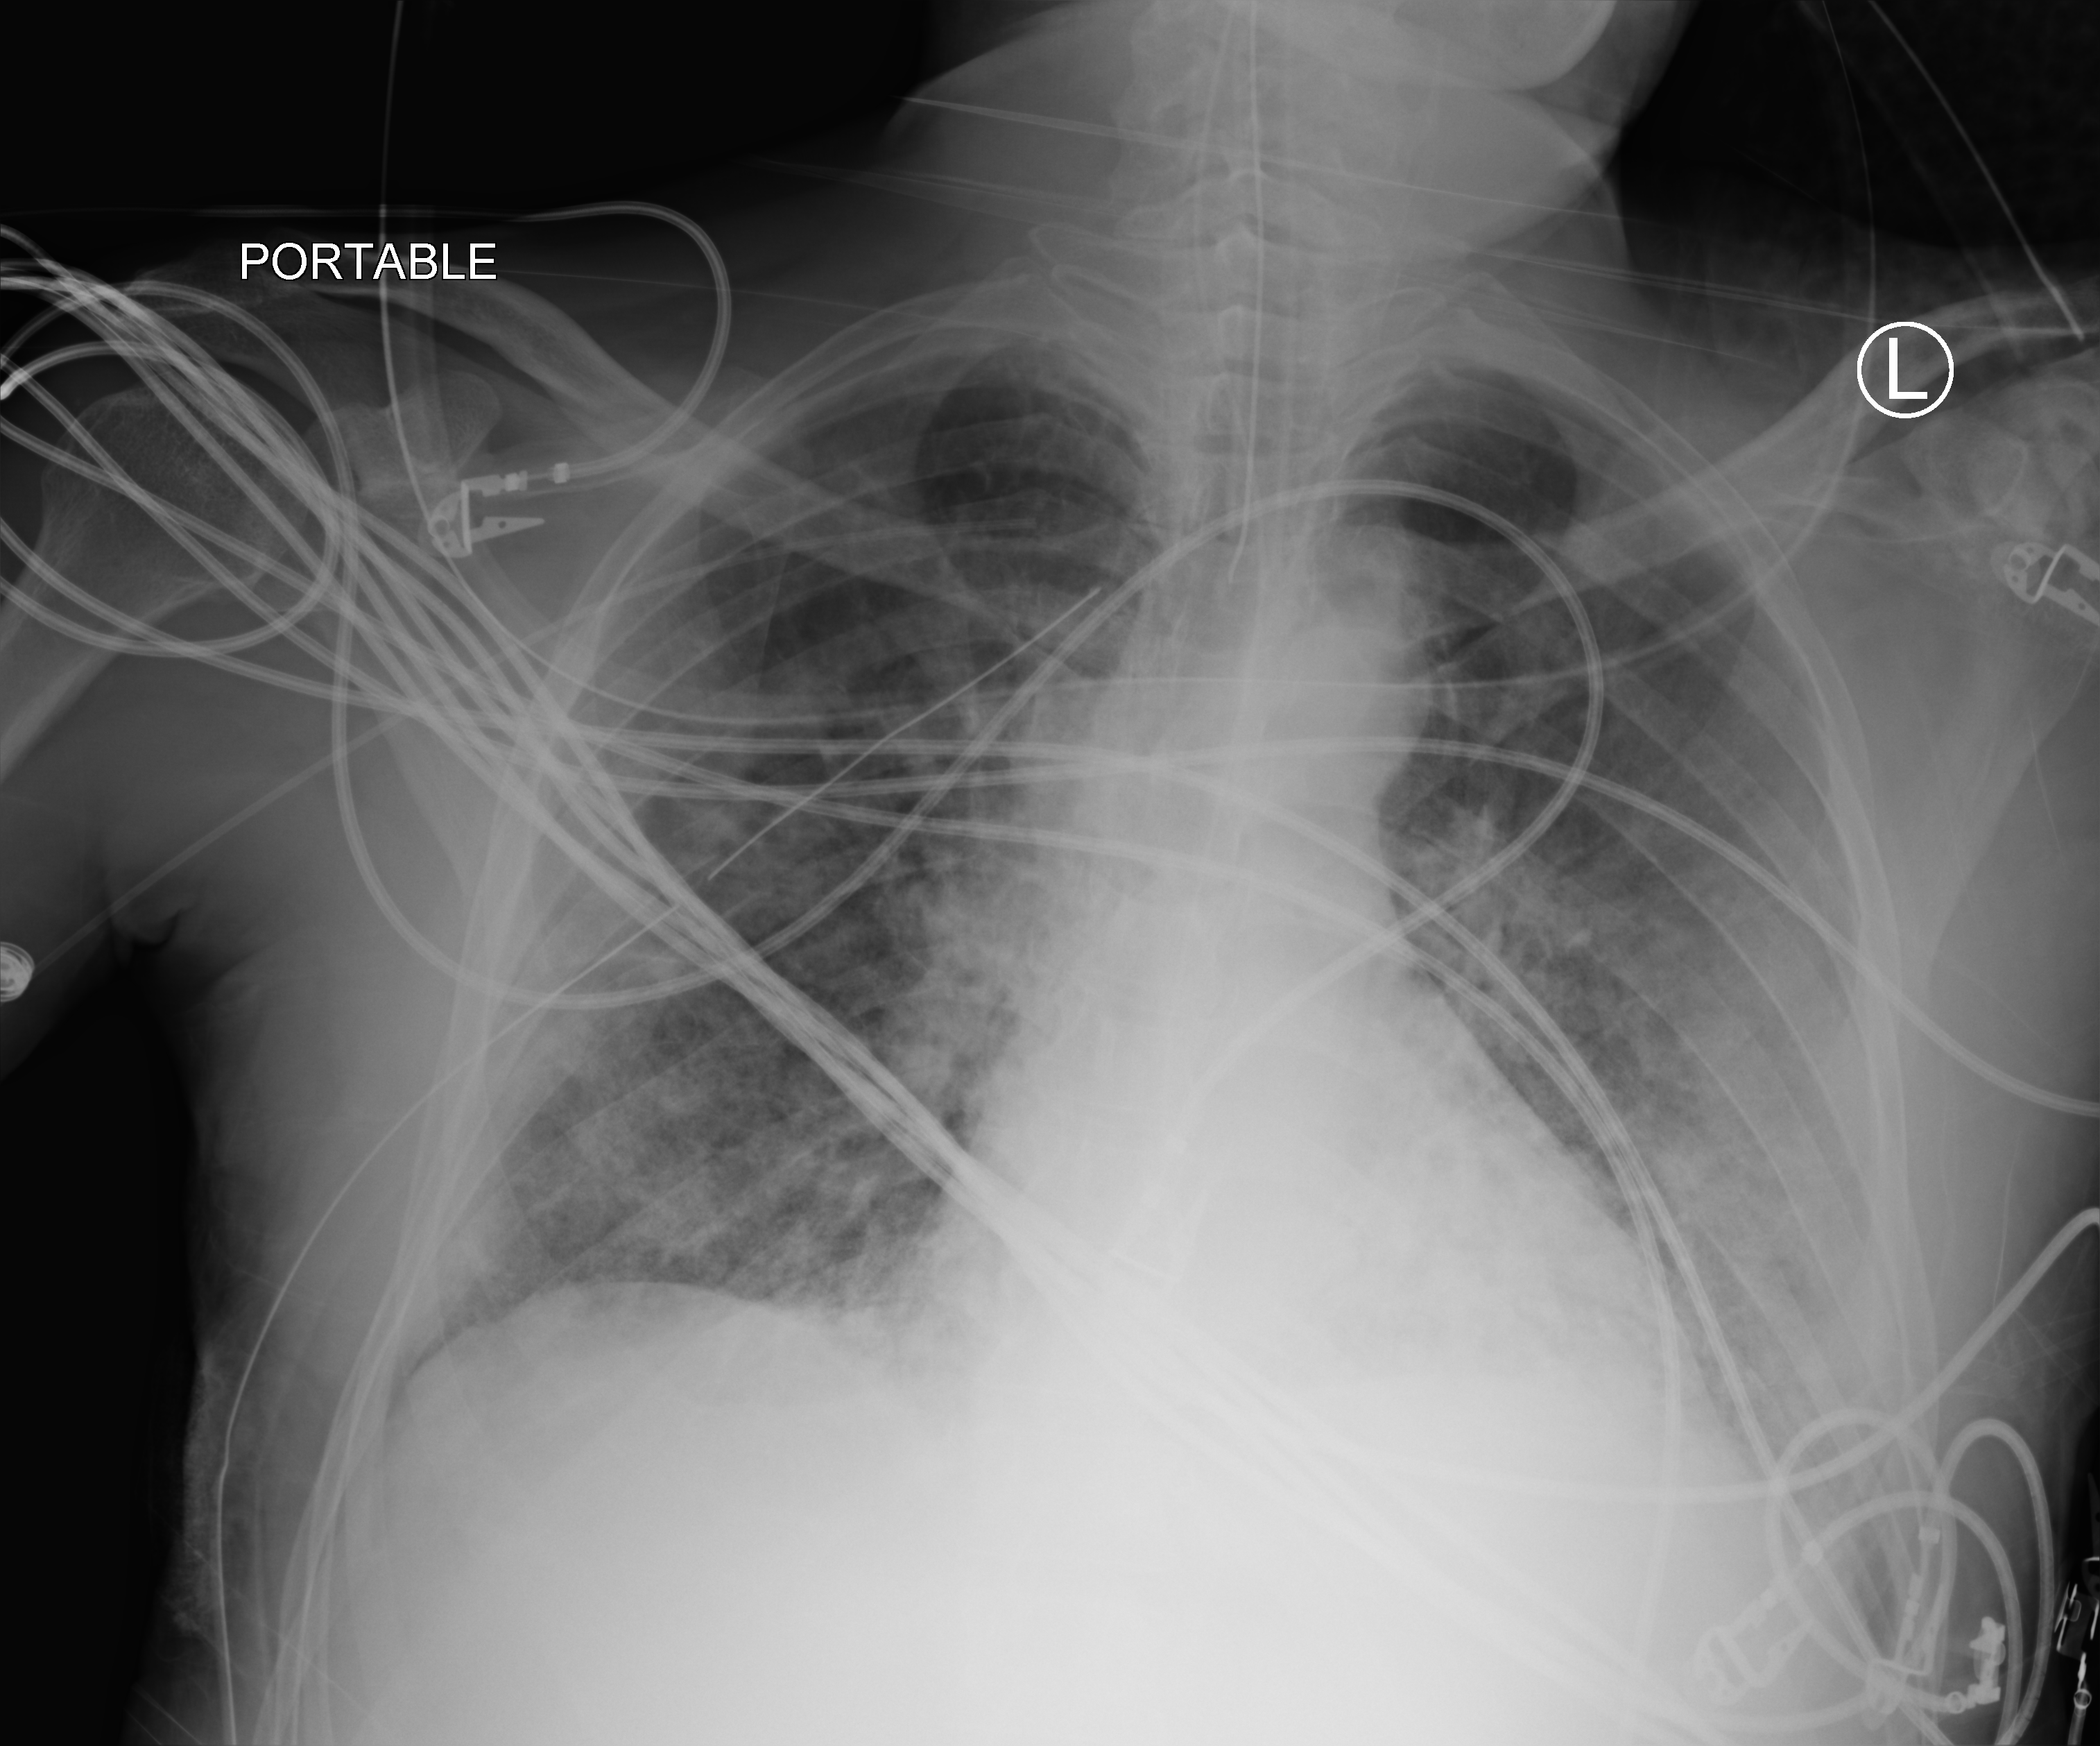
Portable chest radiograph, anteroposterior (AP) projection. Patient hospitalised with COVID-19; male, aged 18–59 years.
From the hospital-stay record, not from the radiograph (when in the stay this image was taken is not recorded): mechanically ventilated during this hospital stay: yes.